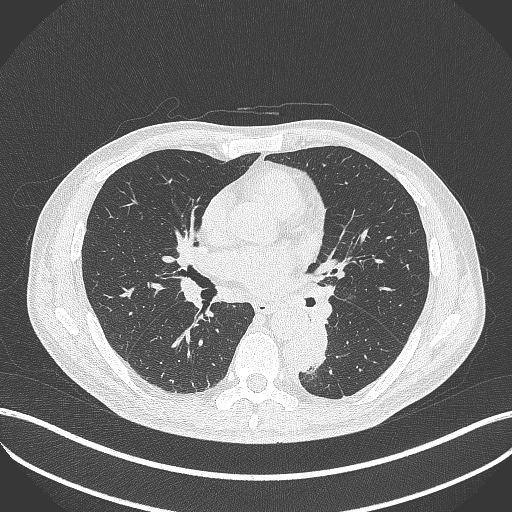
Chest CT, one axial slice. Slice 210 of 451 in the series (ordered by position). Reconstruction kernel B70f. 120 kVp. Lung window (W 1500 / L -600 HU). 1 mm slice thickness. 512 × 512 image matrix, field of view 400 × 400 mm. Male patient, age 72 years. Case-level facts recorded for this patient, not image findings: clinical TNM (as recorded): T2b N0 M1.
Annotated regions visible in this slice (bounding box drawn by a radiologist):
- lung tumour (recorded histology: adenocarcinoma): bounding box [x1, y1, x2, y2] px = [281, 320, 329, 376]